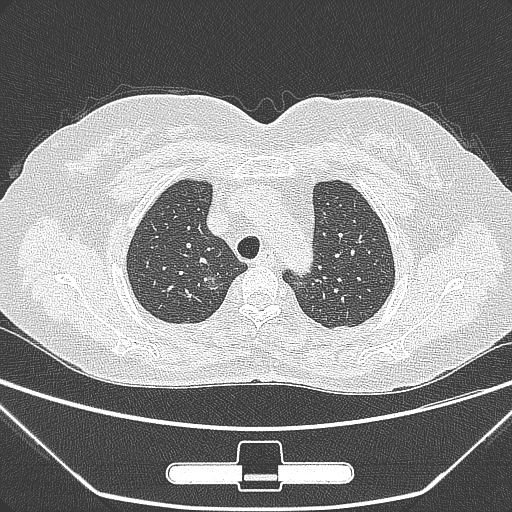
Chest CT, one axial slice. Slice 225 of 275 in the series (ordered by position). Lung window (W 1500 / L -600 HU). 1 mm slice thickness. 512 × 512 image matrix, field of view 356 × 356 mm. Female patient, age 63 years. Case-level facts recorded for this patient, not image findings: clinical TNM (as recorded): T1a N0 M0; histopathological grade: G1.
Outlined on this slice (rectangle marked by the reading radiologist):
- lung tumour (recorded histology: adenocarcinoma): bounding box (x1, y1, x2, y2) in pixels: (189, 262, 224, 295)